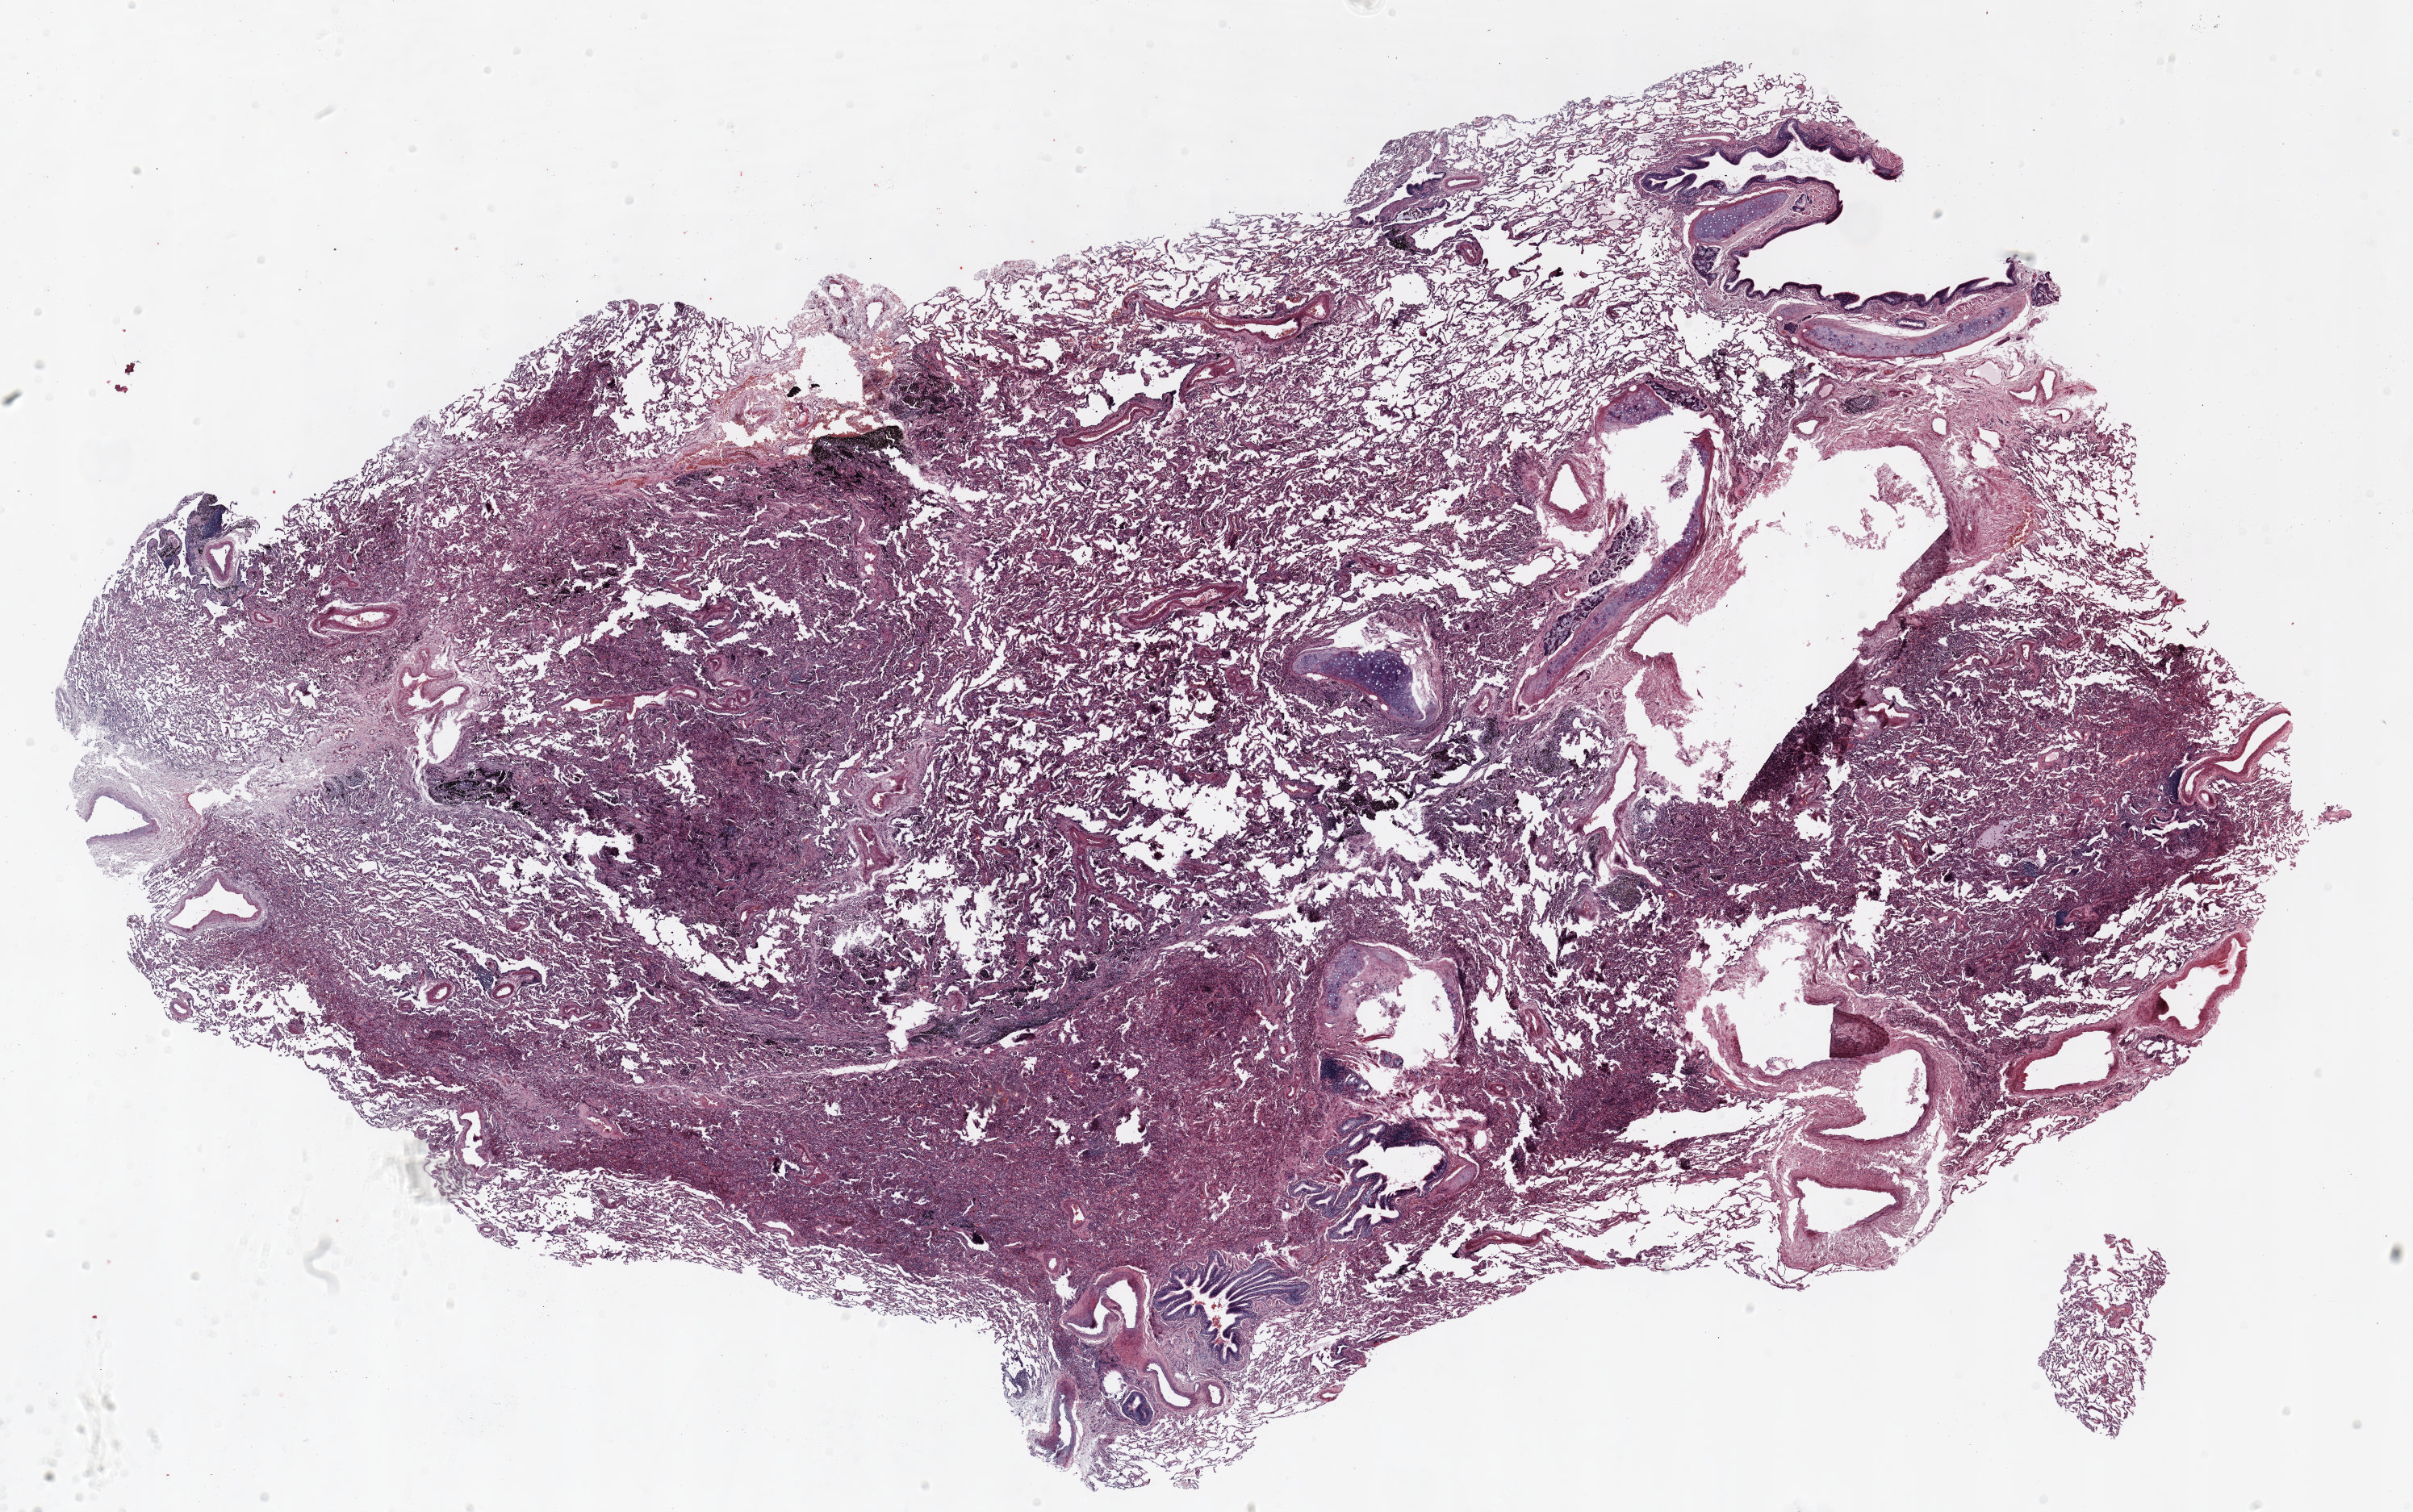
Whole-slide histology image, H&E — shown as a low-resolution overview of the whole scanned area (about 24.0 x 15.1 mm). Formalin-fixed paraffin-embedded (FFPE) section. Lung tissue. Female patient, aged 58 at enrolment. Grade: poorly differentiated (G3).
Stage (AJCC 6th edition): IA. Primary tumour location (clinical record): right lower lobe. Tumour size (pathology): 25 mm. Participant's lung-cancer diagnosis: Non-small cell carcinoma (ICD-O-3 8046/3).